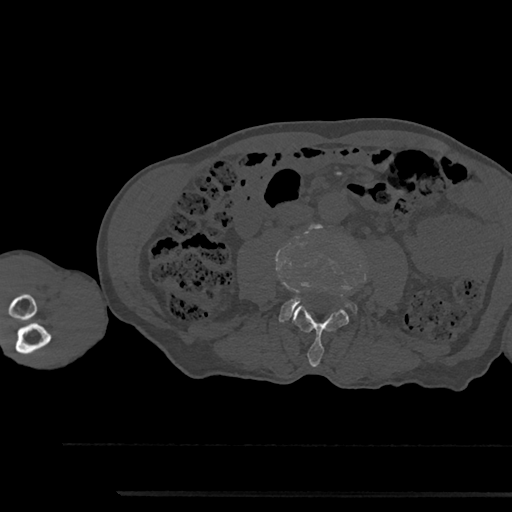
CT including the spine, one axial slice; slice 454 of 797 in the series (ordered by position); reconstruction kernel Br40s/3; bone window (W 1800 / L 400 HU); 512 × 512 image matrix. Male patient, age 79 years. From the clinical record (not read from this slice): primary cancer: prostate.
Annotated regions visible in this slice (semi-automatically segmented with operator editing):
- L3 vertebra: bounding box [x1, y1, x2, y2] px = [293, 306, 349, 367]
- L4 vertebra: [280, 283, 357, 322]